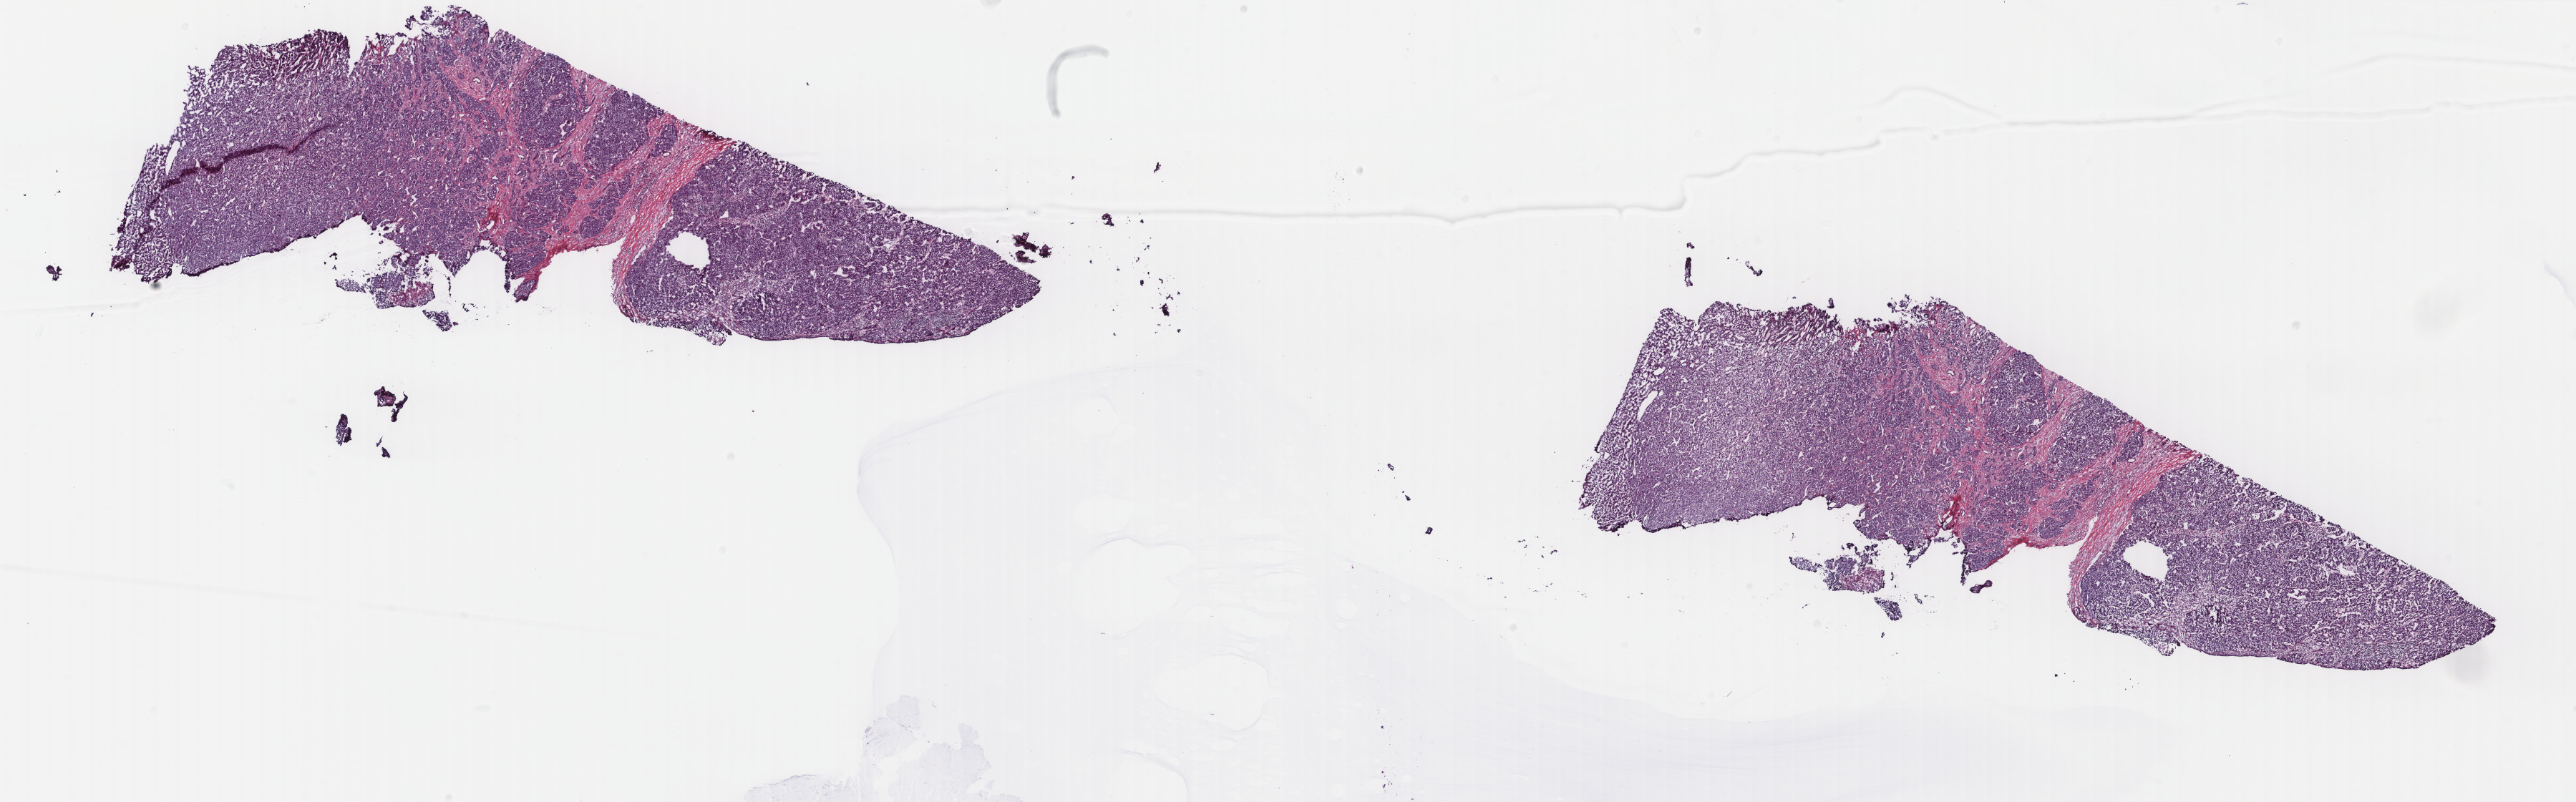
Whole-slide histology image, H&E-stained — low-resolution overview of the scanned area, about 28.6 x 8.9 mm (slide scanned at 40x); frozen section from the top of the tissue portion; primary tumour sample from the liver. Female patient; age at initial diagnosis 52 years. Histologic grade: G3 (poorly differentiated). Composition of this section per pathologist review: tumour cells 100%, tumour nuclei 92%, normal cells 0%, stromal cells 0%, necrosis 0%. Infiltration values recorded for this section: lymphocyte infiltration 0%, monocyte infiltration 0%, neutrophil infiltration 0%.
Diagnosis: Hepatocellular carcinoma, NOS. AJCC pathologic stage: I (6th edition).